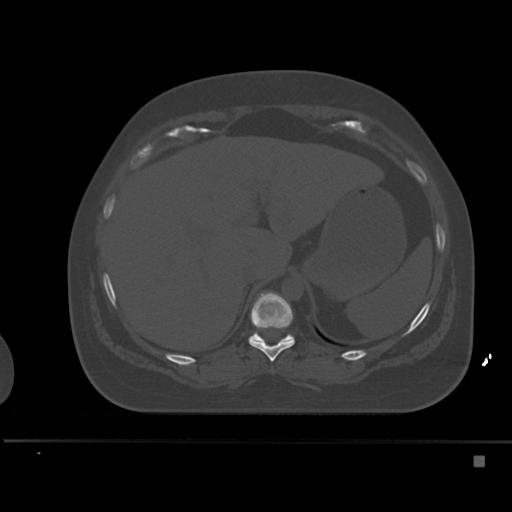
CT including the spine, one axial slice; slice 243 of 495 in the series (ordered by position); bone window (W 1800 / L 400 HU); 1.5 mm slice thickness; 512 × 512 image matrix, field of view 404 × 404 mm. Patient: female, 33 years. Case-level facts recorded for this patient, not image findings: primary cancer: breast; vertebrae with lytic lesions (as recorded): T1.
Outlined on this slice (semi-automatically segmented with operator editing):
- T10 vertebra: box from (x=248, y=292) to (x=295, y=362) px
- T11 vertebra: (x=250, y=333)–(x=294, y=342)